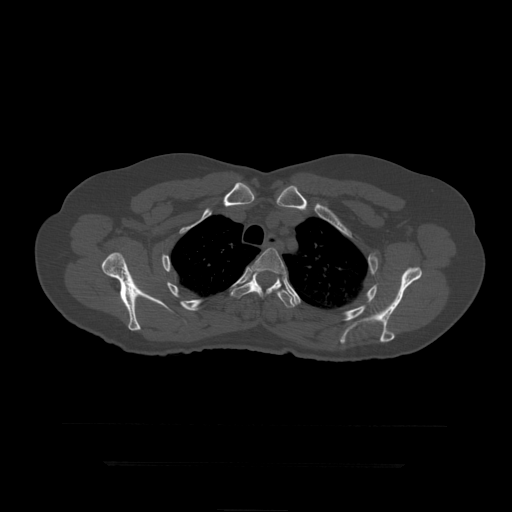
CT including the spine, one axial slice; slice 342 of 399 in the series (ordered by position); reconstruction kernel STANDARD; bone window (W 1800 / L 400 HU); 1.25 mm slice thickness; 512 × 512 image matrix. Patient age 41 years. Case-level facts recorded for this patient, not image findings: primary cancer: breast.
Annotated regions visible in this slice (semi-automatic segmentation, software-assisted and operator-edited):
- T4 vertebra: bounding box (x1, y1, x2, y2) in pixels: (252, 248, 286, 293)
- T5 vertebra: (230, 271, 295, 309)